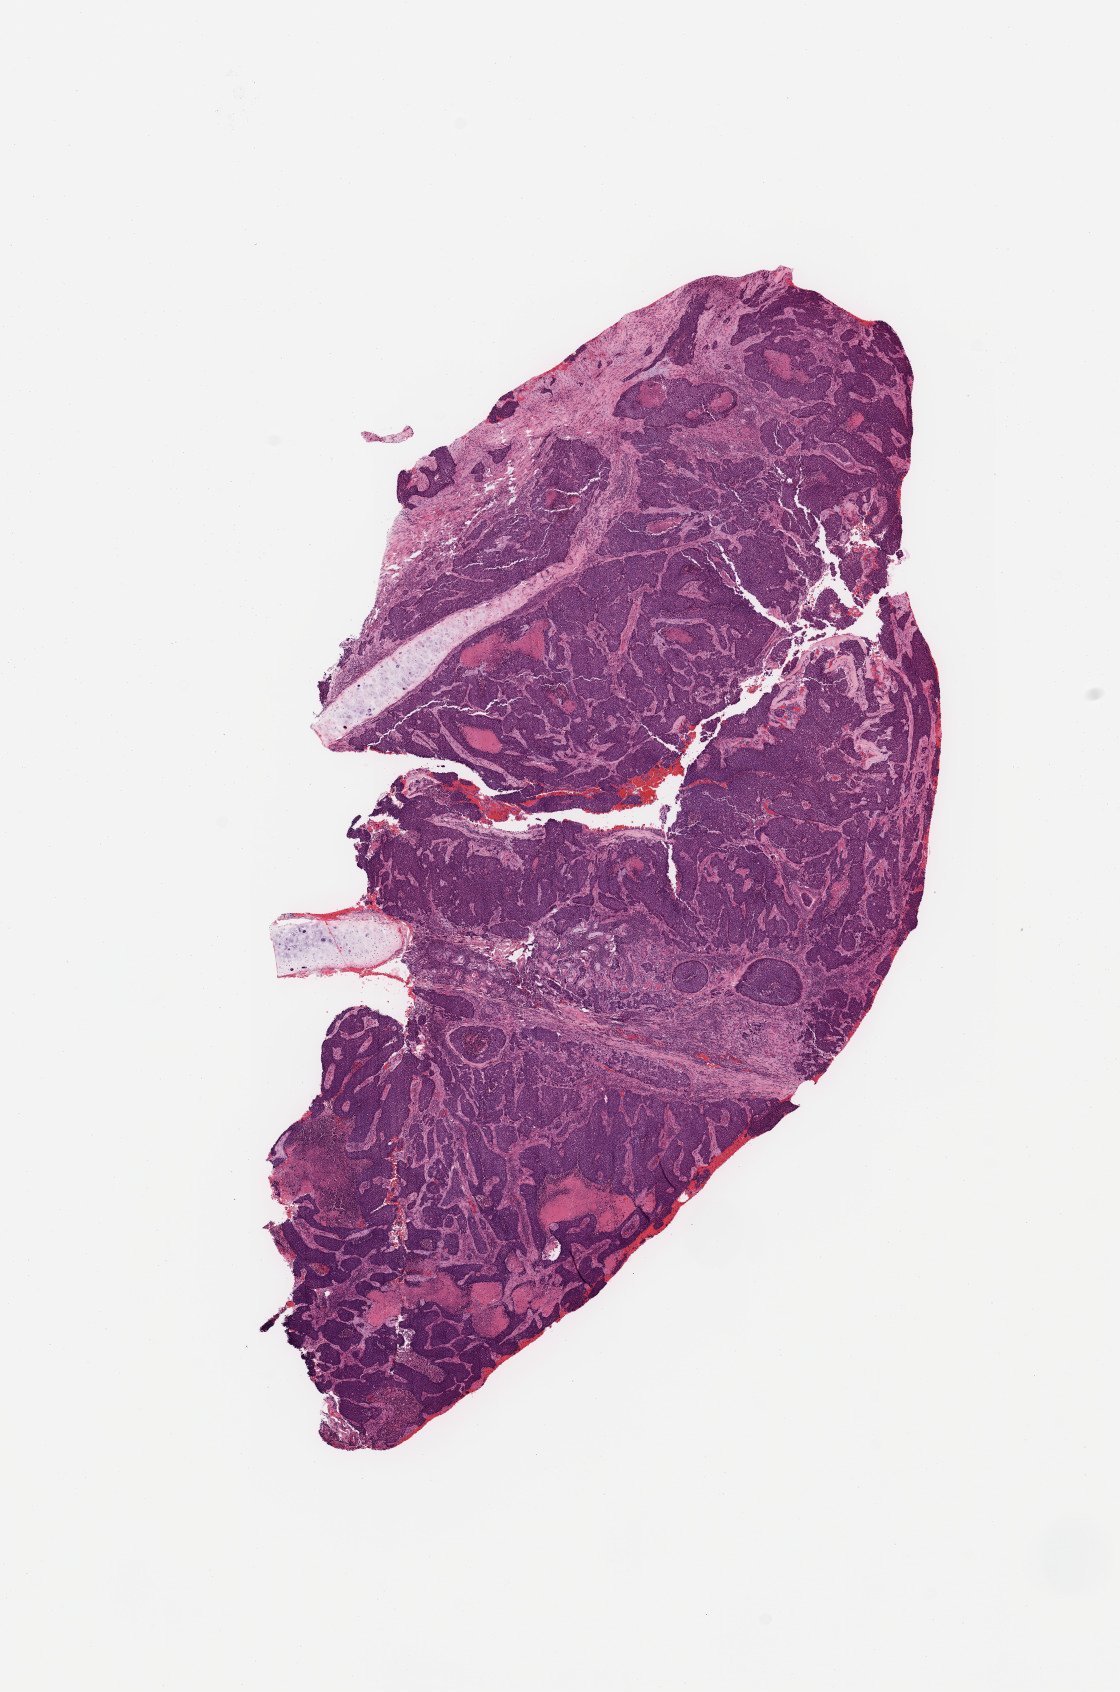
Whole-slide histology image, Hematoxylin and eosin (H&E) stained, low-resolution overview of the scanned area, about 8.9 x 13.4 mm; tumour tissue sample, lung. Patient: male, age 54 years. Histologic grade: G2 (moderately differentiated).
* diagnosis: Squamous cell carcinoma, NOS
* AJCC pathologic stage: IIA
* primary tumour site (as recorded): left upper lobe